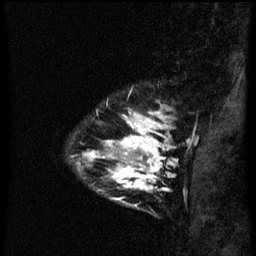
Breast MRI (dynamic contrast-enhanced), one sagittal slice; position 13 of 60 along the scan axis; dynamic contrast-enhanced series, image 2 of 3 at this slice position (ordered by acquisition); 1.5 T; TE 4.2 ms, TR 8 ms; 2.3 mm slice thickness; 256 × 256 image matrix, field of view 180 × 180 mm. Female patient, age 33 years.
Outlined on this slice (semi-automatically segmented with operator editing):
- analysis volume of interest (the breast-tissue region the enhancement analysis was run in; not a lesion): bounding box [x1, y1, x2, y2] px = [78, 118, 171, 209]
- tumour enhancement mask (voxels above the 70 % enhancement threshold inside the analysis volume of interest): [89, 118, 169, 191]